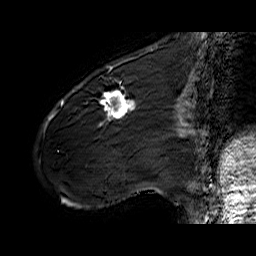
Breast MRI (dynamic contrast-enhanced), one sagittal slice. Slice 18 of 60 in the series (ordered by position). Dynamic contrast-enhanced series, time point 2 of 6 at this slice position (early post-contrast). 1.5 T. TE 6.4 ms, TR 32.9 ms. 4 mm slice thickness. 256 × 256 image matrix, field of view 200 × 200 mm. Female patient. Case-level facts recorded for this patient, not image findings: setting: breast cancer imaged before/during neoadjuvant chemotherapy; receptor status: HER2-positive.
Structures marked on this image (semi-automatically segmented with operator editing):
- analysis volume of interest (the breast-tissue region the enhancement analysis was run in; not a lesion): box from (x=61, y=77) to (x=141, y=142) px
- tumour enhancement mask (voxels above the 100 % enhancement threshold inside the analysis volume of interest): (x=61, y=90)–(x=136, y=126)